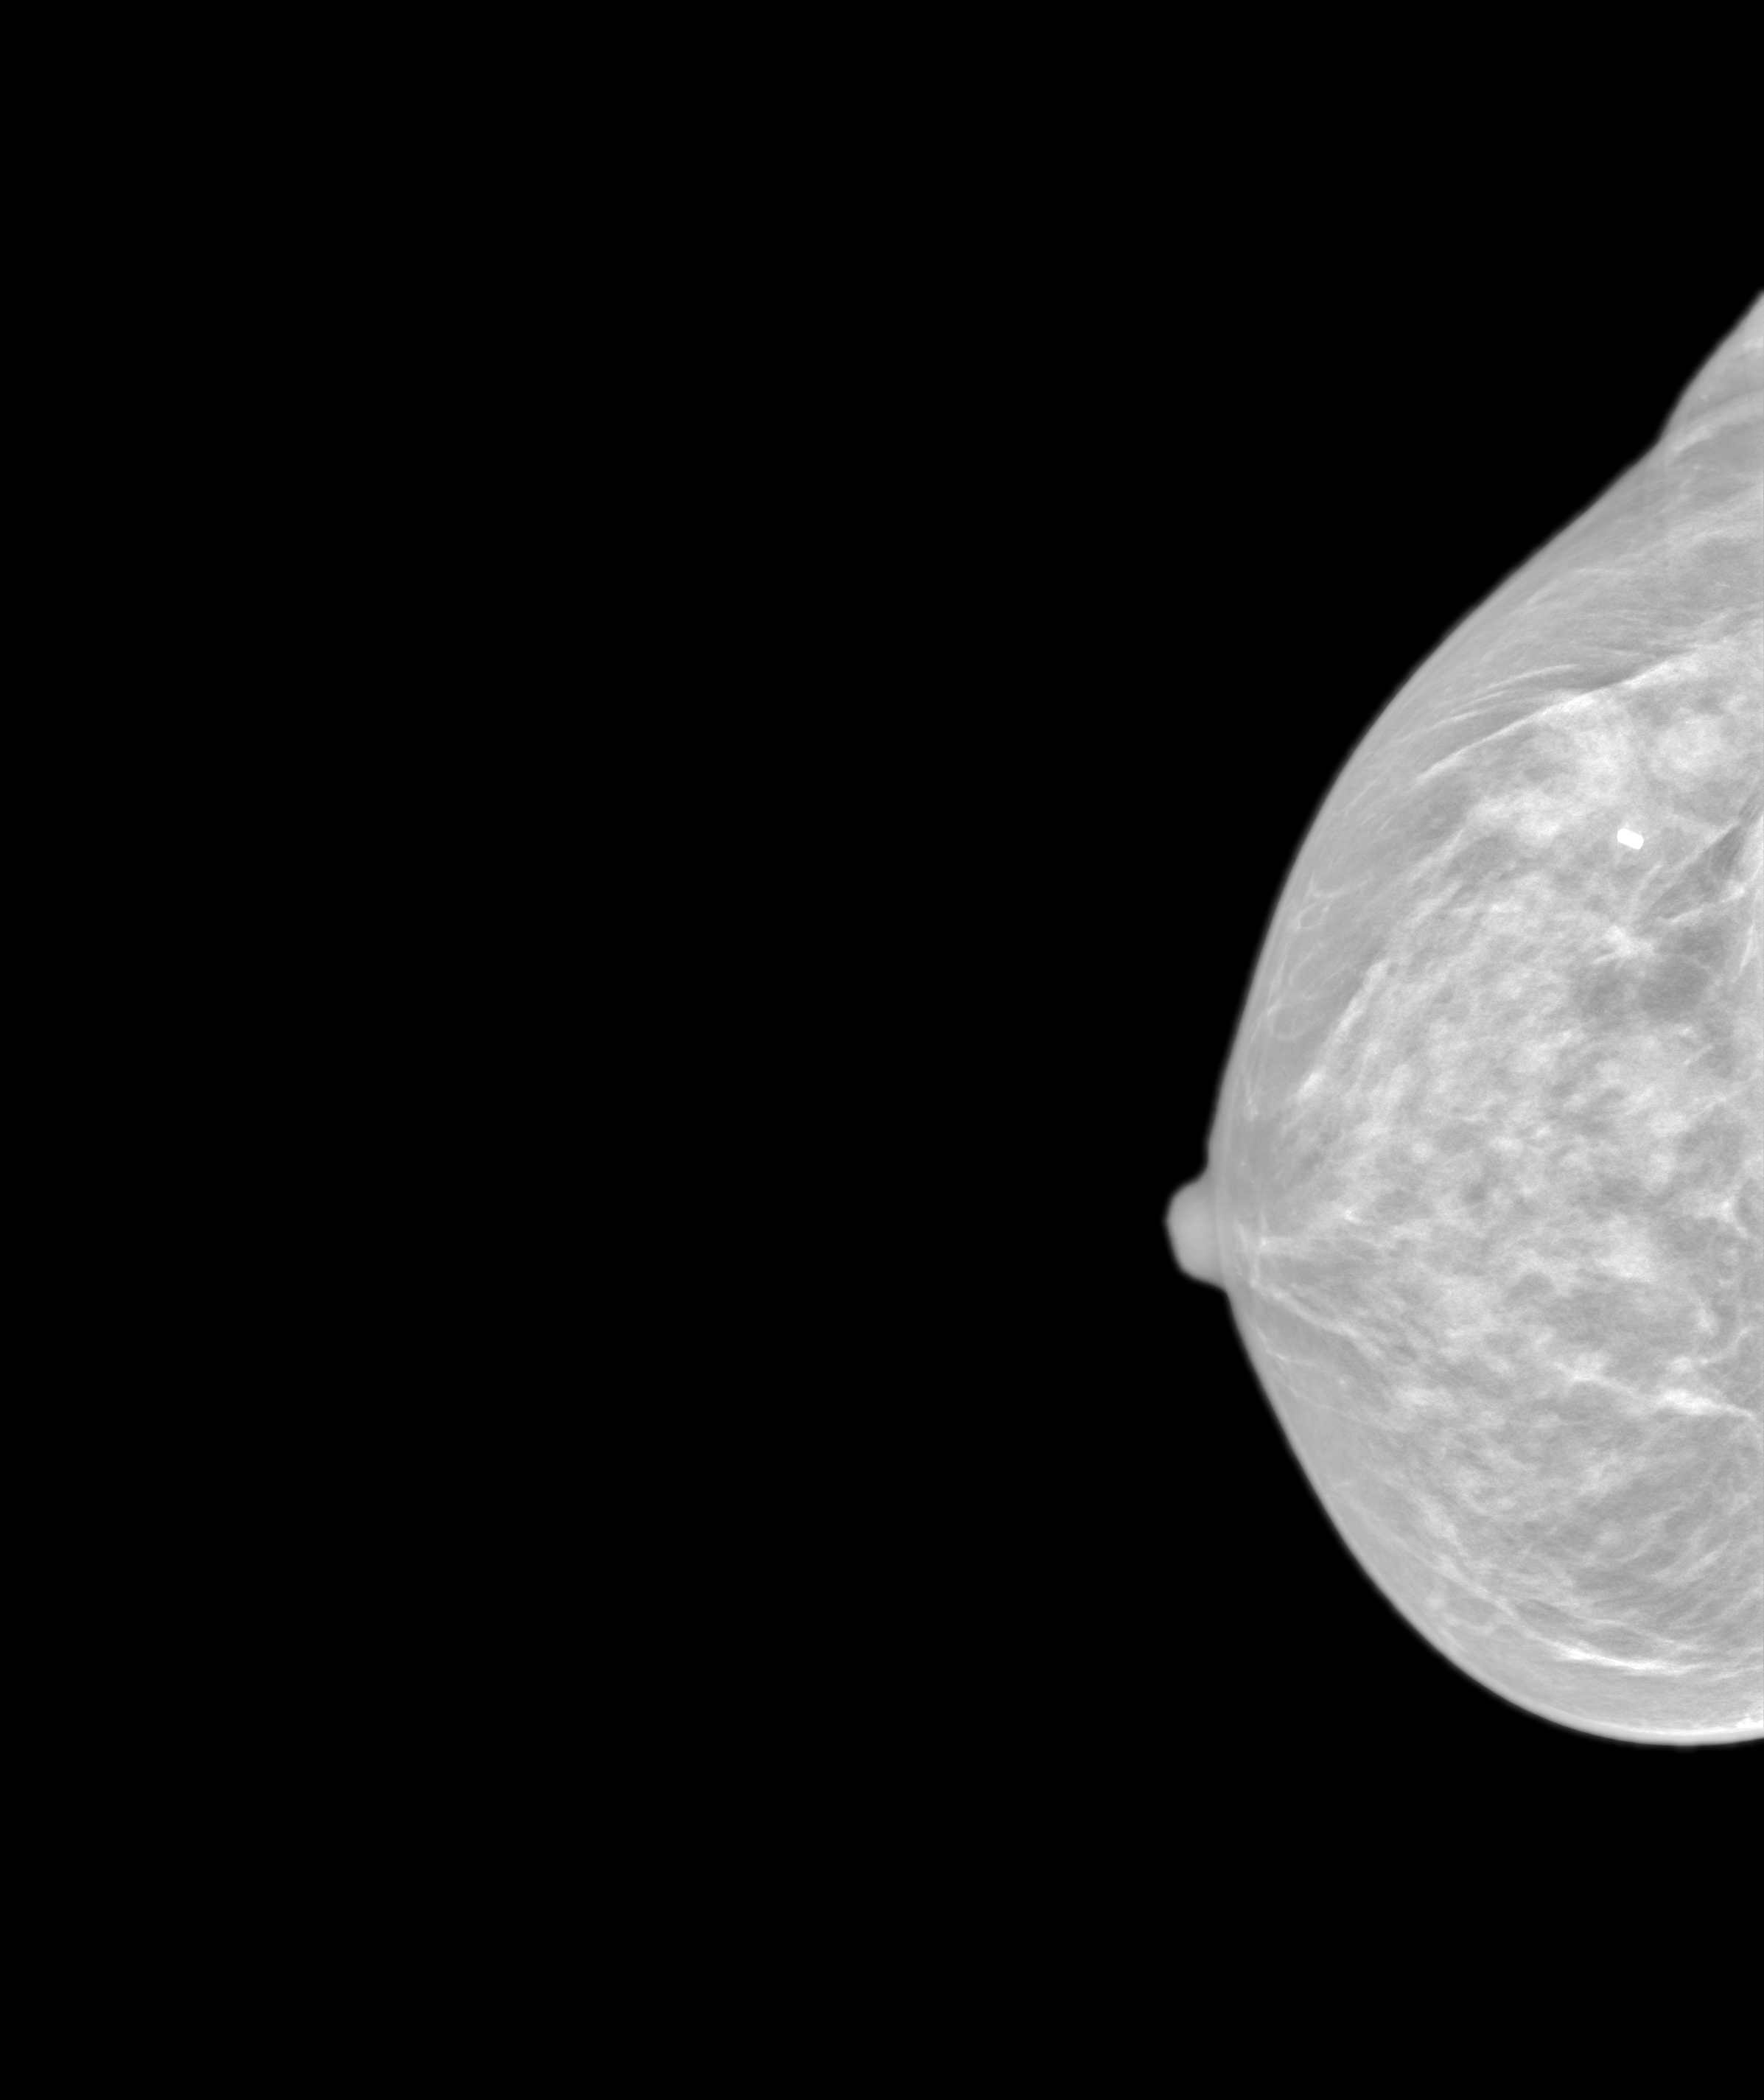
Annual screening mammography examination; system: SenoIris_1SP2(440). Female patient, age 57 years.
Image type: synthesized 2-D view from tomosynthesis. Breast: right. Projection: craniocaudal (CC) view.